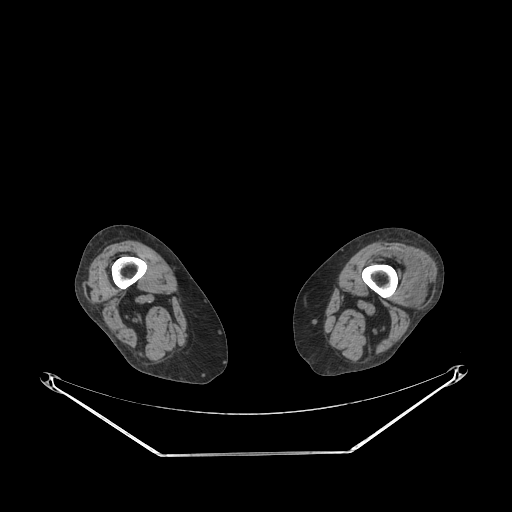
CT of an extremity soft-tissue mass (from a PET/CT study), one axial slice; reconstruction kernel STANDARD; 140 kVp; soft-tissue window (W 400 / L 40 HU); 3.75 mm slice thickness; 512 × 512 image matrix, field of view 500 × 500 mm. Female patient. From the clinical record (not read from this slice): histological type: undifferentiated – high grade; grade: high; site of the primary tumour: left thigh.
Outlined on this slice (expert contour drawn on MRI and transferred to this co-registered scan by the dataset authors):
- gross tumour volume including surrounding oedema: bounding box <404,278,421,291> (left, top, right, bottom; pixels)